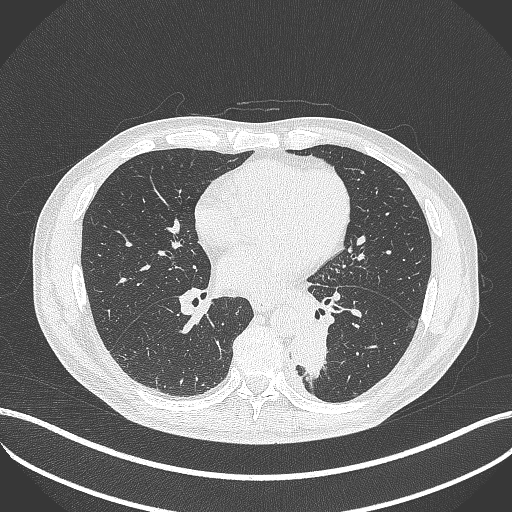
Chest CT, one axial slice. Slice 184 of 451 in the series (ordered by position). 120 kVp. Lung window (W 1500 / L -600 HU). 512 × 512 image matrix, field of view 400 × 400 mm. Male patient, age 72 years. From the clinical record (not read from this slice): clinical TNM (as recorded): T2b N0 M1.
Outlined on this slice (bounding box drawn by a radiologist):
- lung tumour (recorded histology: adenocarcinoma): box from (x=289, y=315) to (x=330, y=386) px